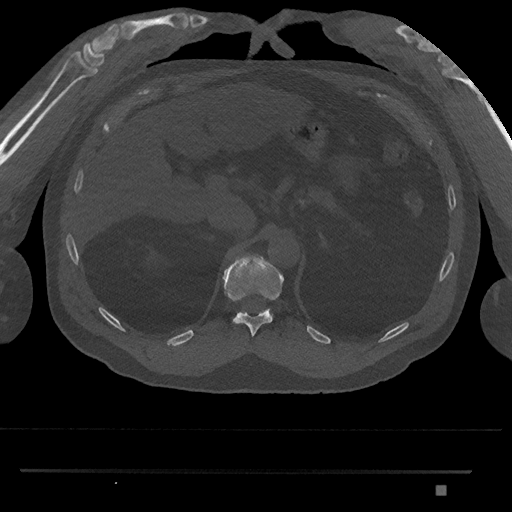
CT including the spine, one axial slice. Reconstruction kernel Br40s/3. 120 kVp. Bone window (W 1800 / L 400 HU). 0.5 mm slice thickness. 512 × 512 image matrix, field of view 429 × 429 mm. Patient: male, 65 years. Case-level facts recorded for this patient, not image findings: primary cancer: prostate.
Annotated regions visible in this slice (semi-automatic segmentation, software-assisted and operator-edited):
- T11 vertebra: bounding box <223,255,284,337> (left, top, right, bottom; pixels)